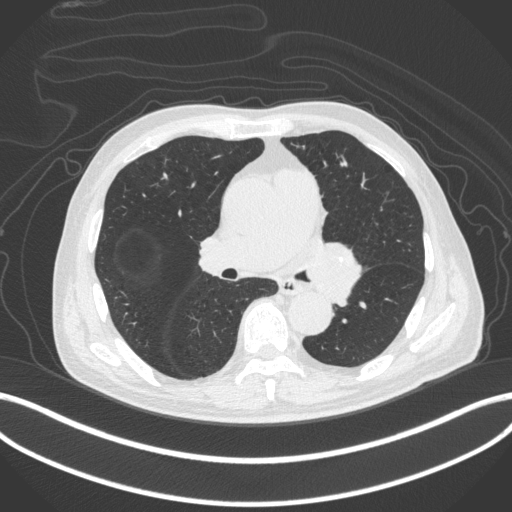
Chest CT, one axial slice. Position 242 of 420 along the scan axis. 120 kVp. Lung window (W 1500 / L -600 HU). 1 mm slice thickness. 512 × 512 image matrix, field of view 400 × 400 mm. Patient: male, 77 years. From the clinical record (not read from this slice): clinical TNM (as recorded): T3 N1 M0.
Outlined on this slice (rectangle marked by the reading radiologist):
- lung tumour (recorded histology: adenocarcinoma): bounding box <304,242,363,304> (left, top, right, bottom; pixels)